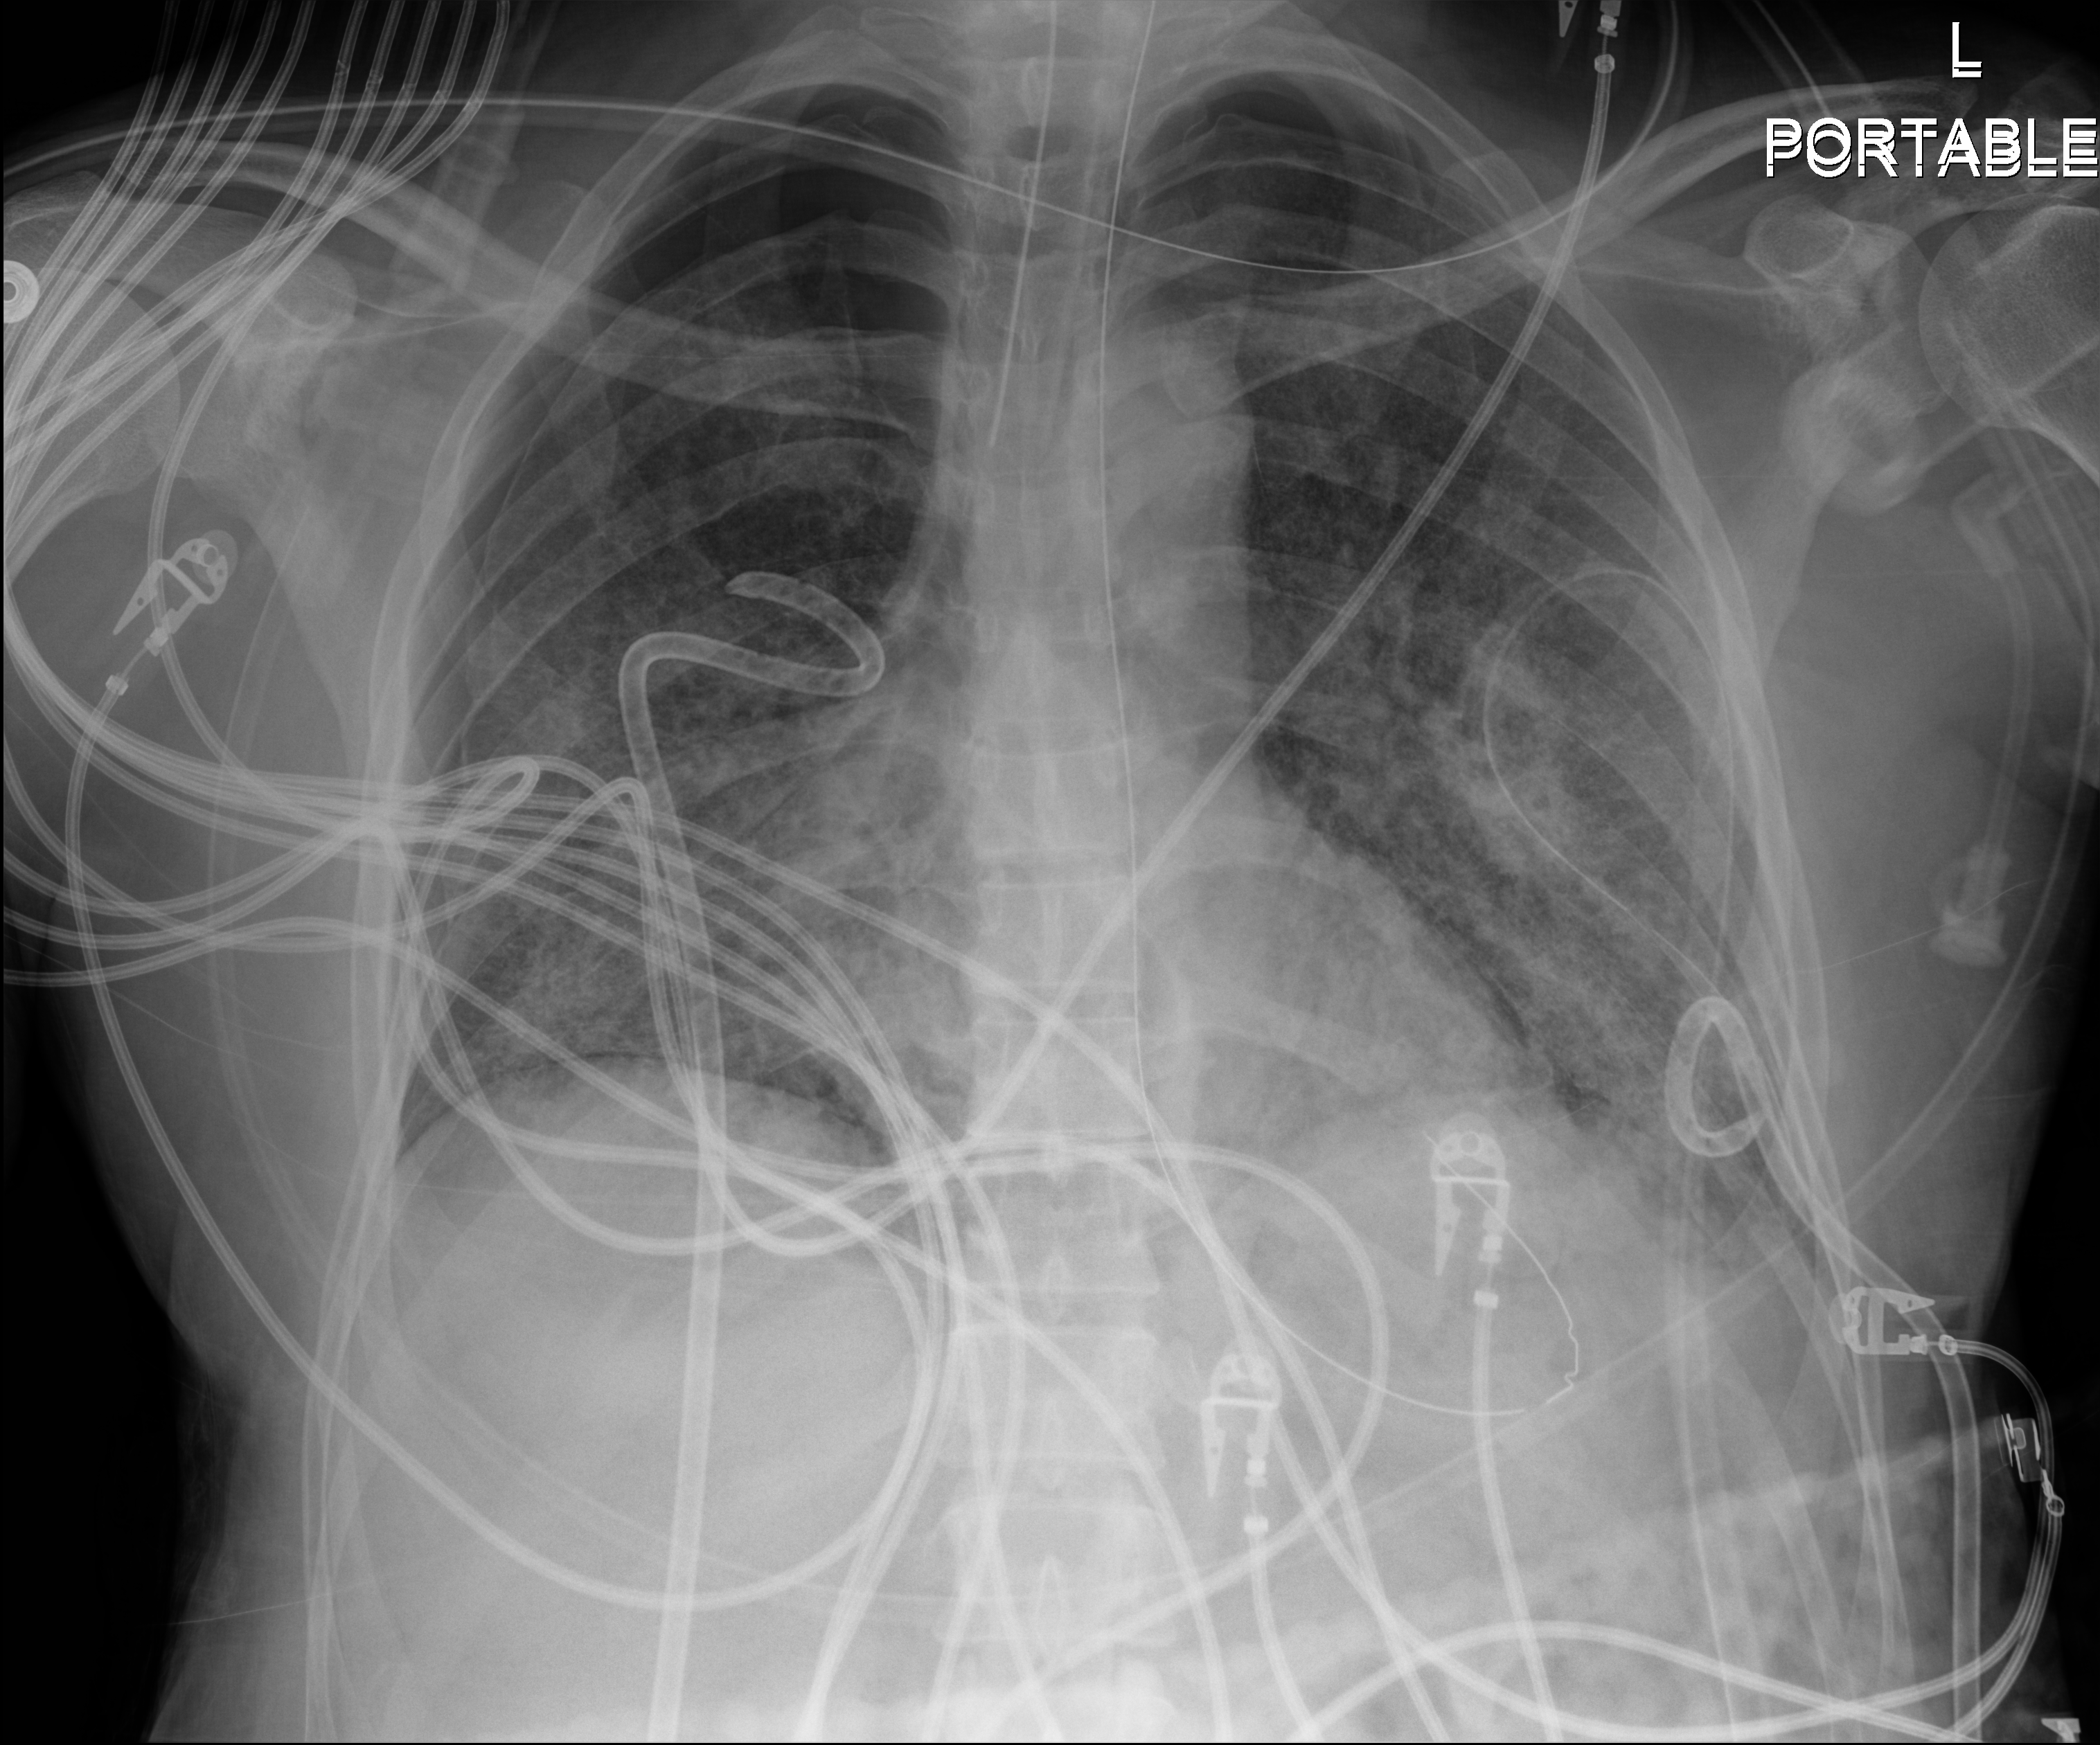
Chest radiograph (digital radiography), anteroposterior (AP) projection. Adult patient hospitalised with COVID-19, age 18–59 years.
From the hospital-stay record, not from the radiograph (when in the stay this image was taken is not recorded): admitted to intensive care during this hospital stay: yes.